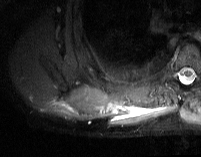
MRI of an extremity soft-tissue mass, one axial slice; slice 15 of 74 in the series (ordered by position); STIR; MR volume resampled by the dataset authors to the PET/CT grid (not the native acquisition matrix); 3.27 mm slice thickness; 201 × 157 image matrix. Male patient. From the clinical record (not read from this slice): histological type: pleiomorphic spindle cell undifferentiated; grade: high; site of the primary tumour: right parascapusular.
Outlined on this slice (expert contour drawn on MRI and transferred to this co-registered scan by the dataset authors):
- gross tumour volume including surrounding oedema: box from (x=65, y=89) to (x=171, y=126) px